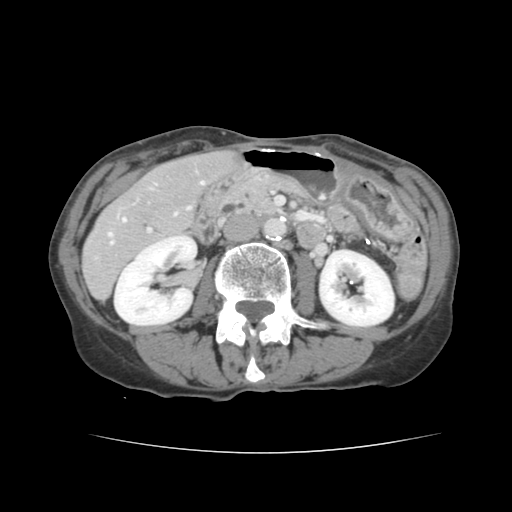
Contrast-enhanced abdominal CT, one axial slice. Slice 52 of 136 in the series (ordered by position). Intravenous contrast given. Soft-tissue window (W 400 / L 40 HU). 2.5 mm slice thickness. 512 × 512 image matrix, field of view 319 × 319 mm. Female patient, age 77 years. Case-level facts recorded for this patient, not image findings: diagnosis: colorectal cancer liver metastases, imaged before liver resection; multiple liver metastases: yes; largest metastasis: 3 cm; chemotherapy before resection: yes.
Outlined on this slice (manually delineated by an expert):
- hepatic veins: bounding box <109,181,204,244> (left, top, right, bottom; pixels)
- liver: <84,152,234,299>
- planned liver remnant (the part of the liver to remain after resection): <168,152,233,194>
- portal vein (with intrahepatic branches): <147,228,151,232>